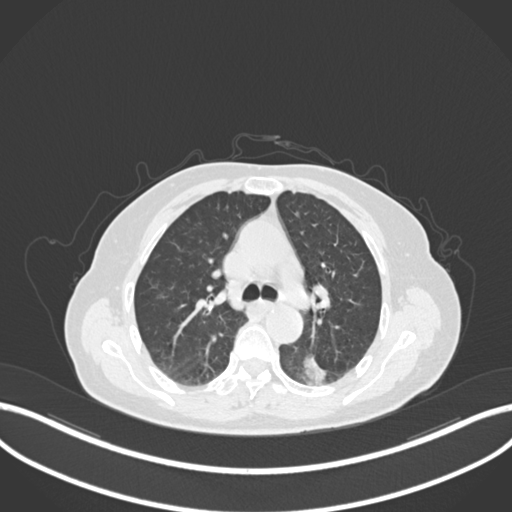
Chest CT, one axial slice; slice 542 of 727 in the series (ordered by position); reconstruction kernel B30f; lung window (W 1500 / L -600 HU); 1 mm slice thickness; 512 × 512 image matrix, field of view 400 × 400 mm. Female patient, age 70 years. Case-level facts recorded for this patient, not image findings: clinical TNM (as recorded): T1c N0 M0.
Outlined on this slice (bounding box drawn by a radiologist):
- lung tumour (recorded histology: adenocarcinoma): bounding box <299,348,331,385> (left, top, right, bottom; pixels)